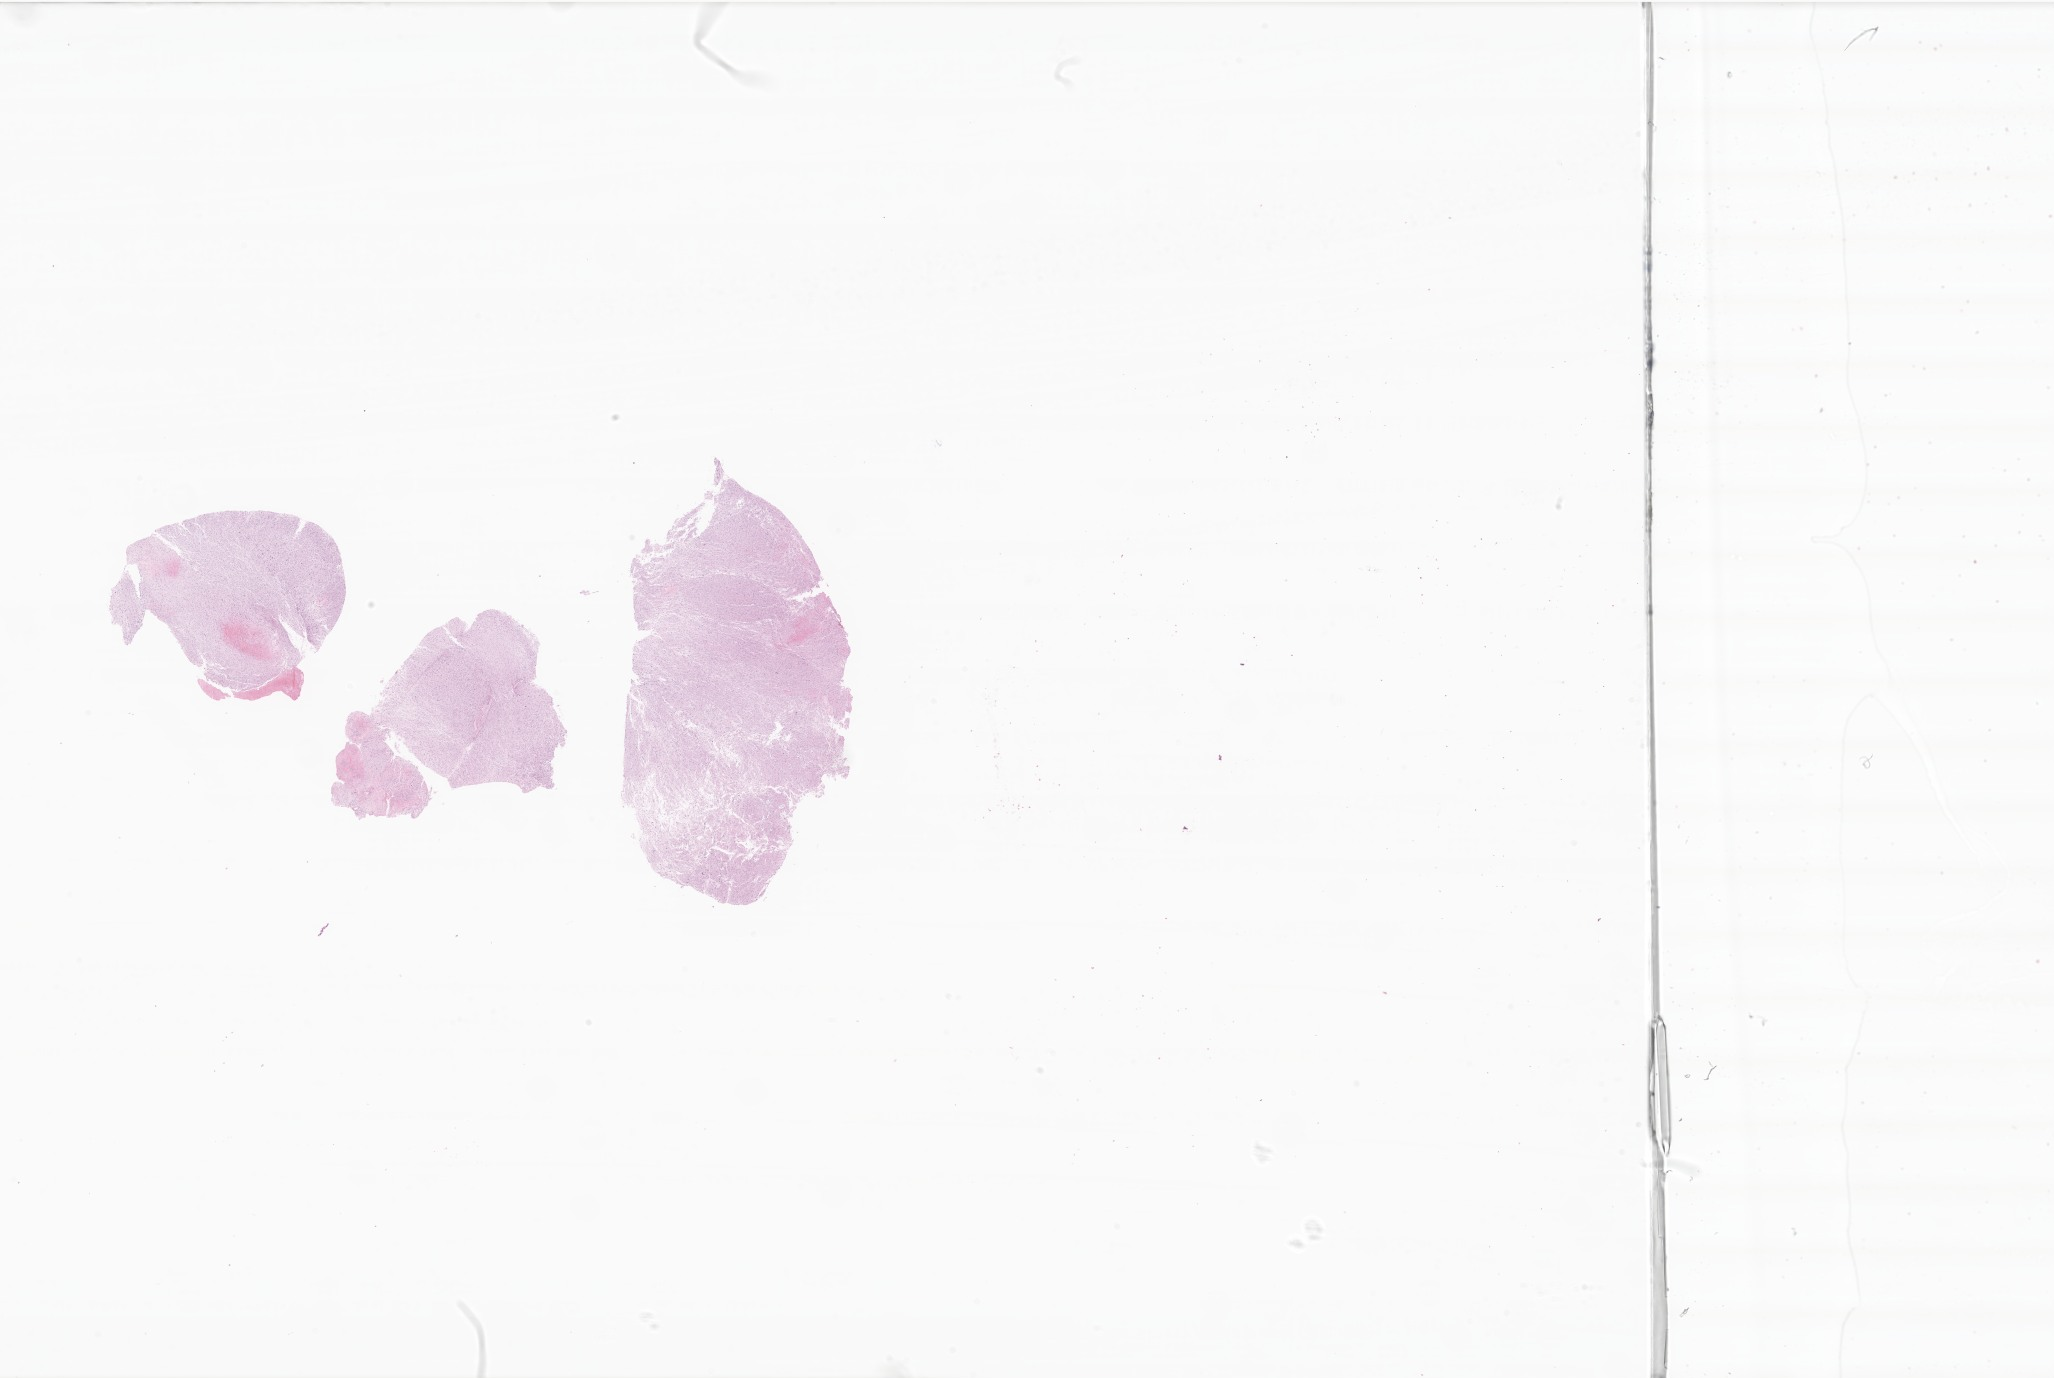
Whole-slide image, haematoxylin and eosin stain of tumor tissue from the brain — whole scanned area (about 34.6 x 23.2 mm) shown as a low-resolution overview. Formalin-fixed, paraffin-embedded (FFPE) tissue. Patient: male, age 113 months (9 years 5 months).
Recorded diagnosis: Glioma, malignant.